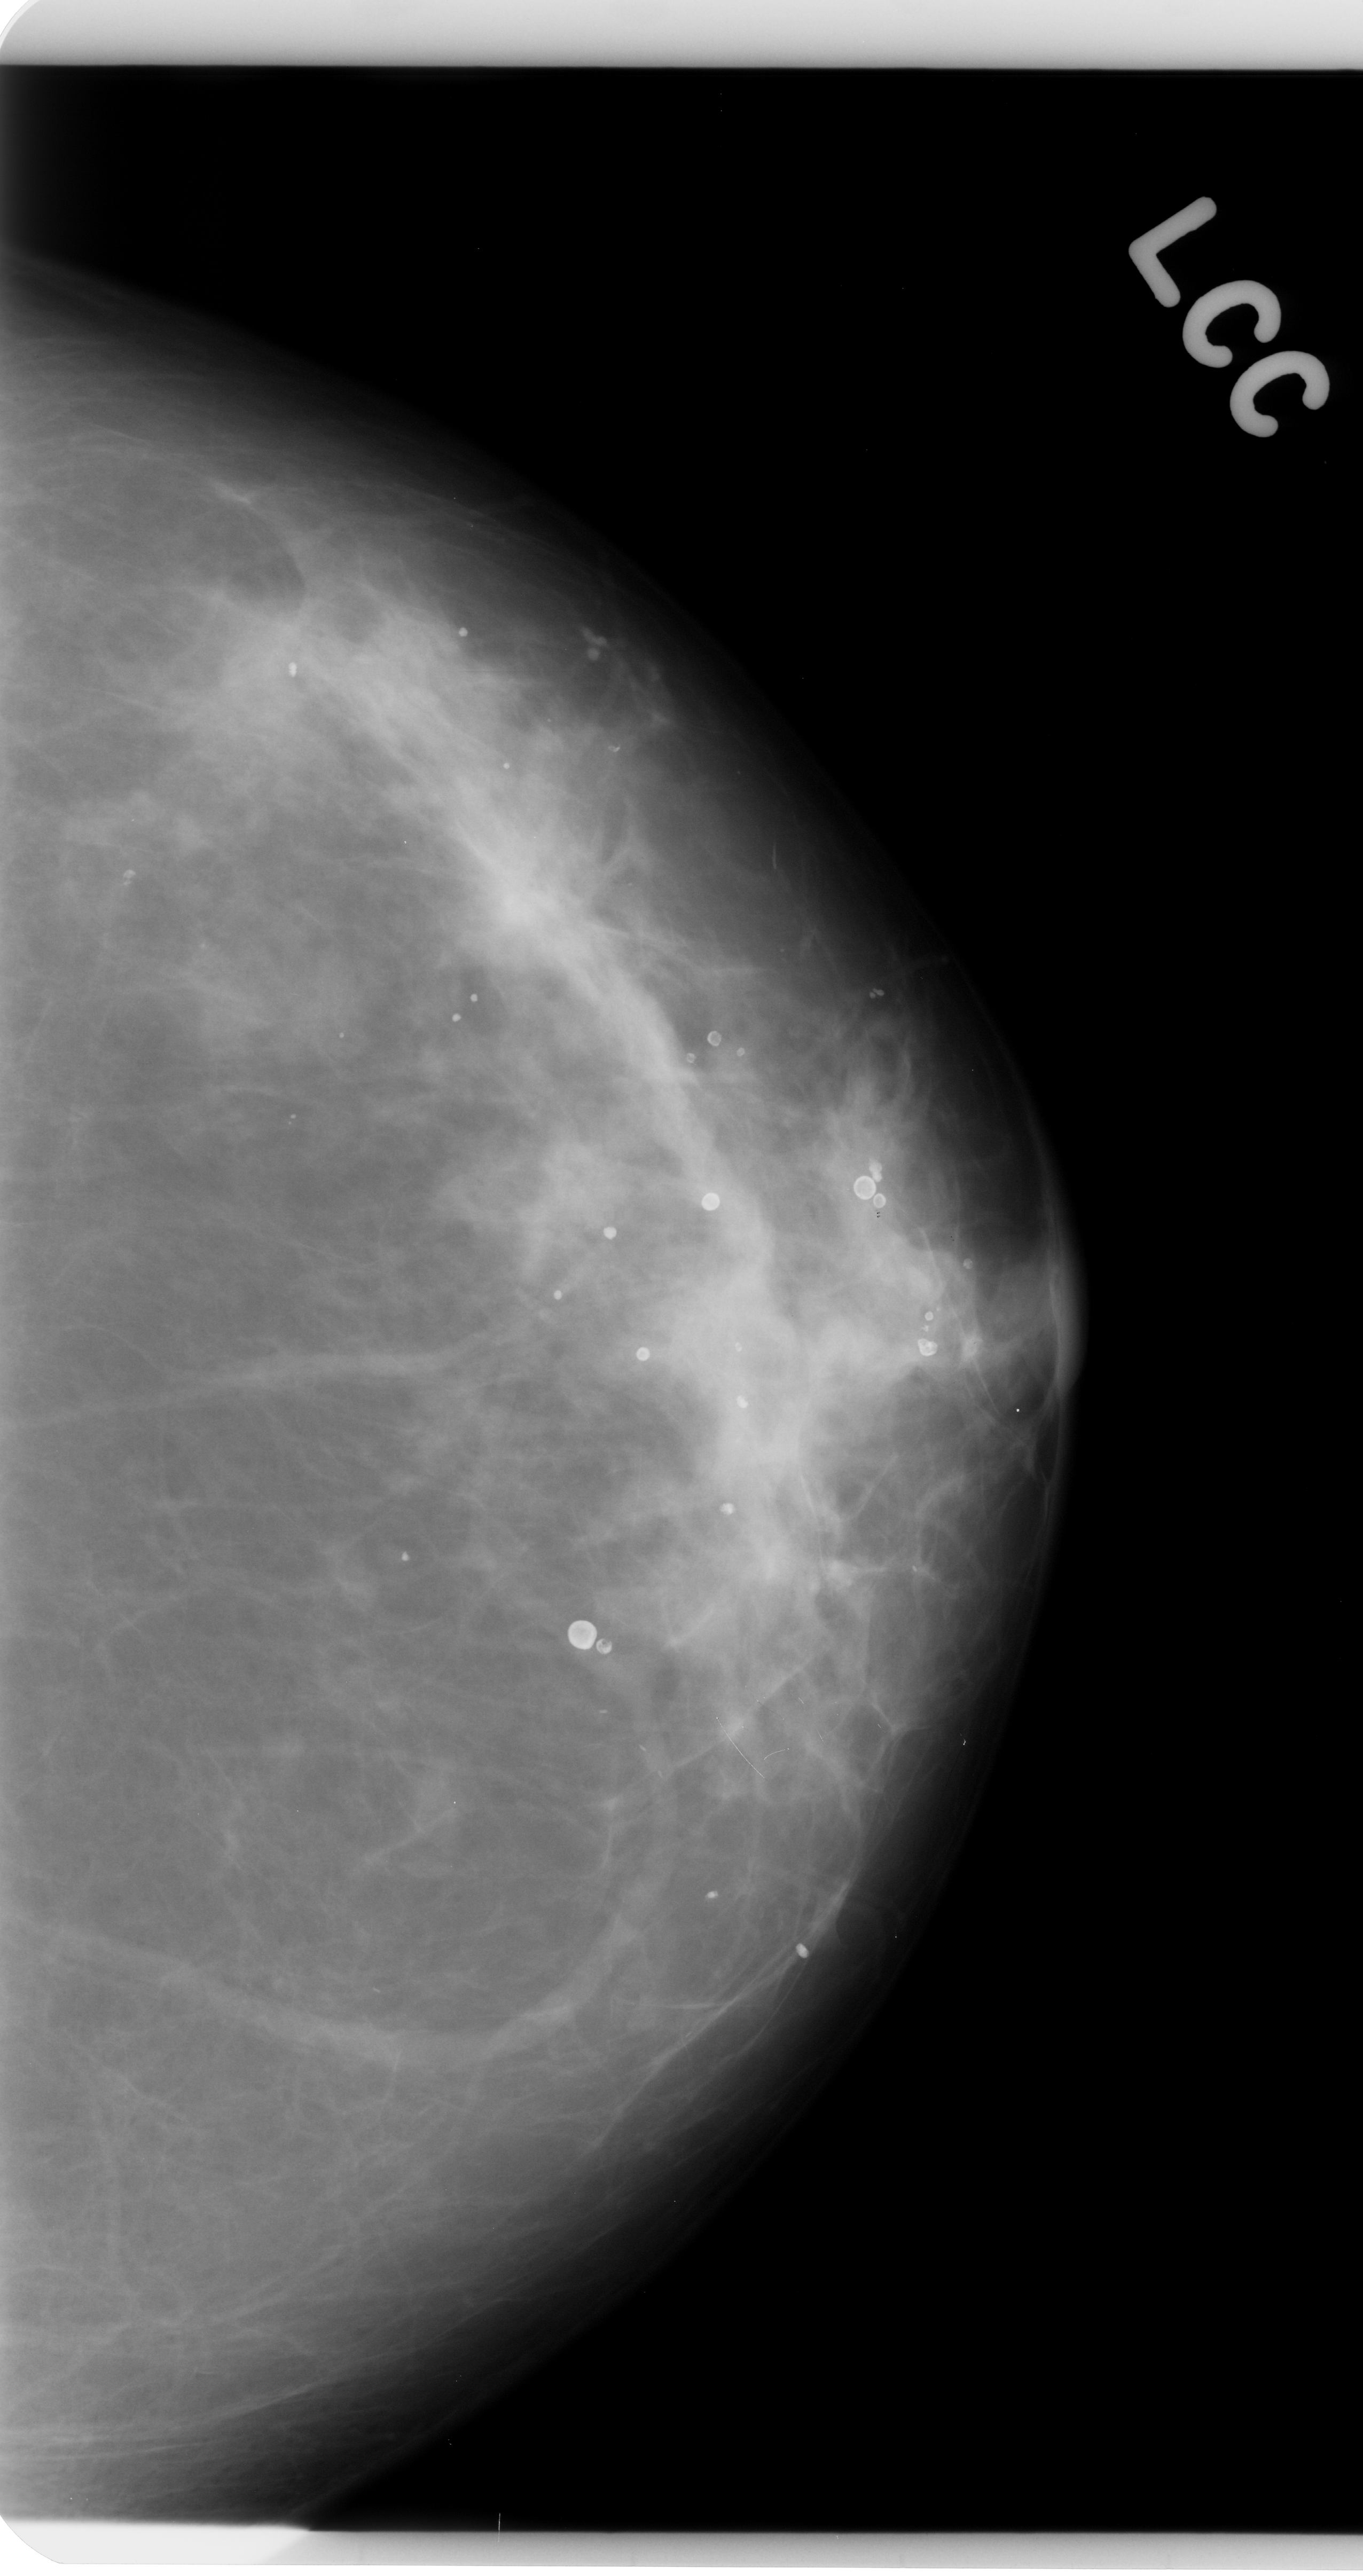
Mammogram (digitized film). Left breast. CC view. BI-RADS breast density category 2 (scale 1–4). 1363 × 2576 image matrix.
Marked abnormalities (boxes around the expert regions of interest):
- mass, shape architectural distortion, margins spiculated; BI-RADS assessment category 4; subtlety rating 5 on a 1 (subtle) to 5 (obvious) scale; pathology result (as recorded, not read from the image): benign: box from (x=452, y=812) to (x=632, y=992) px